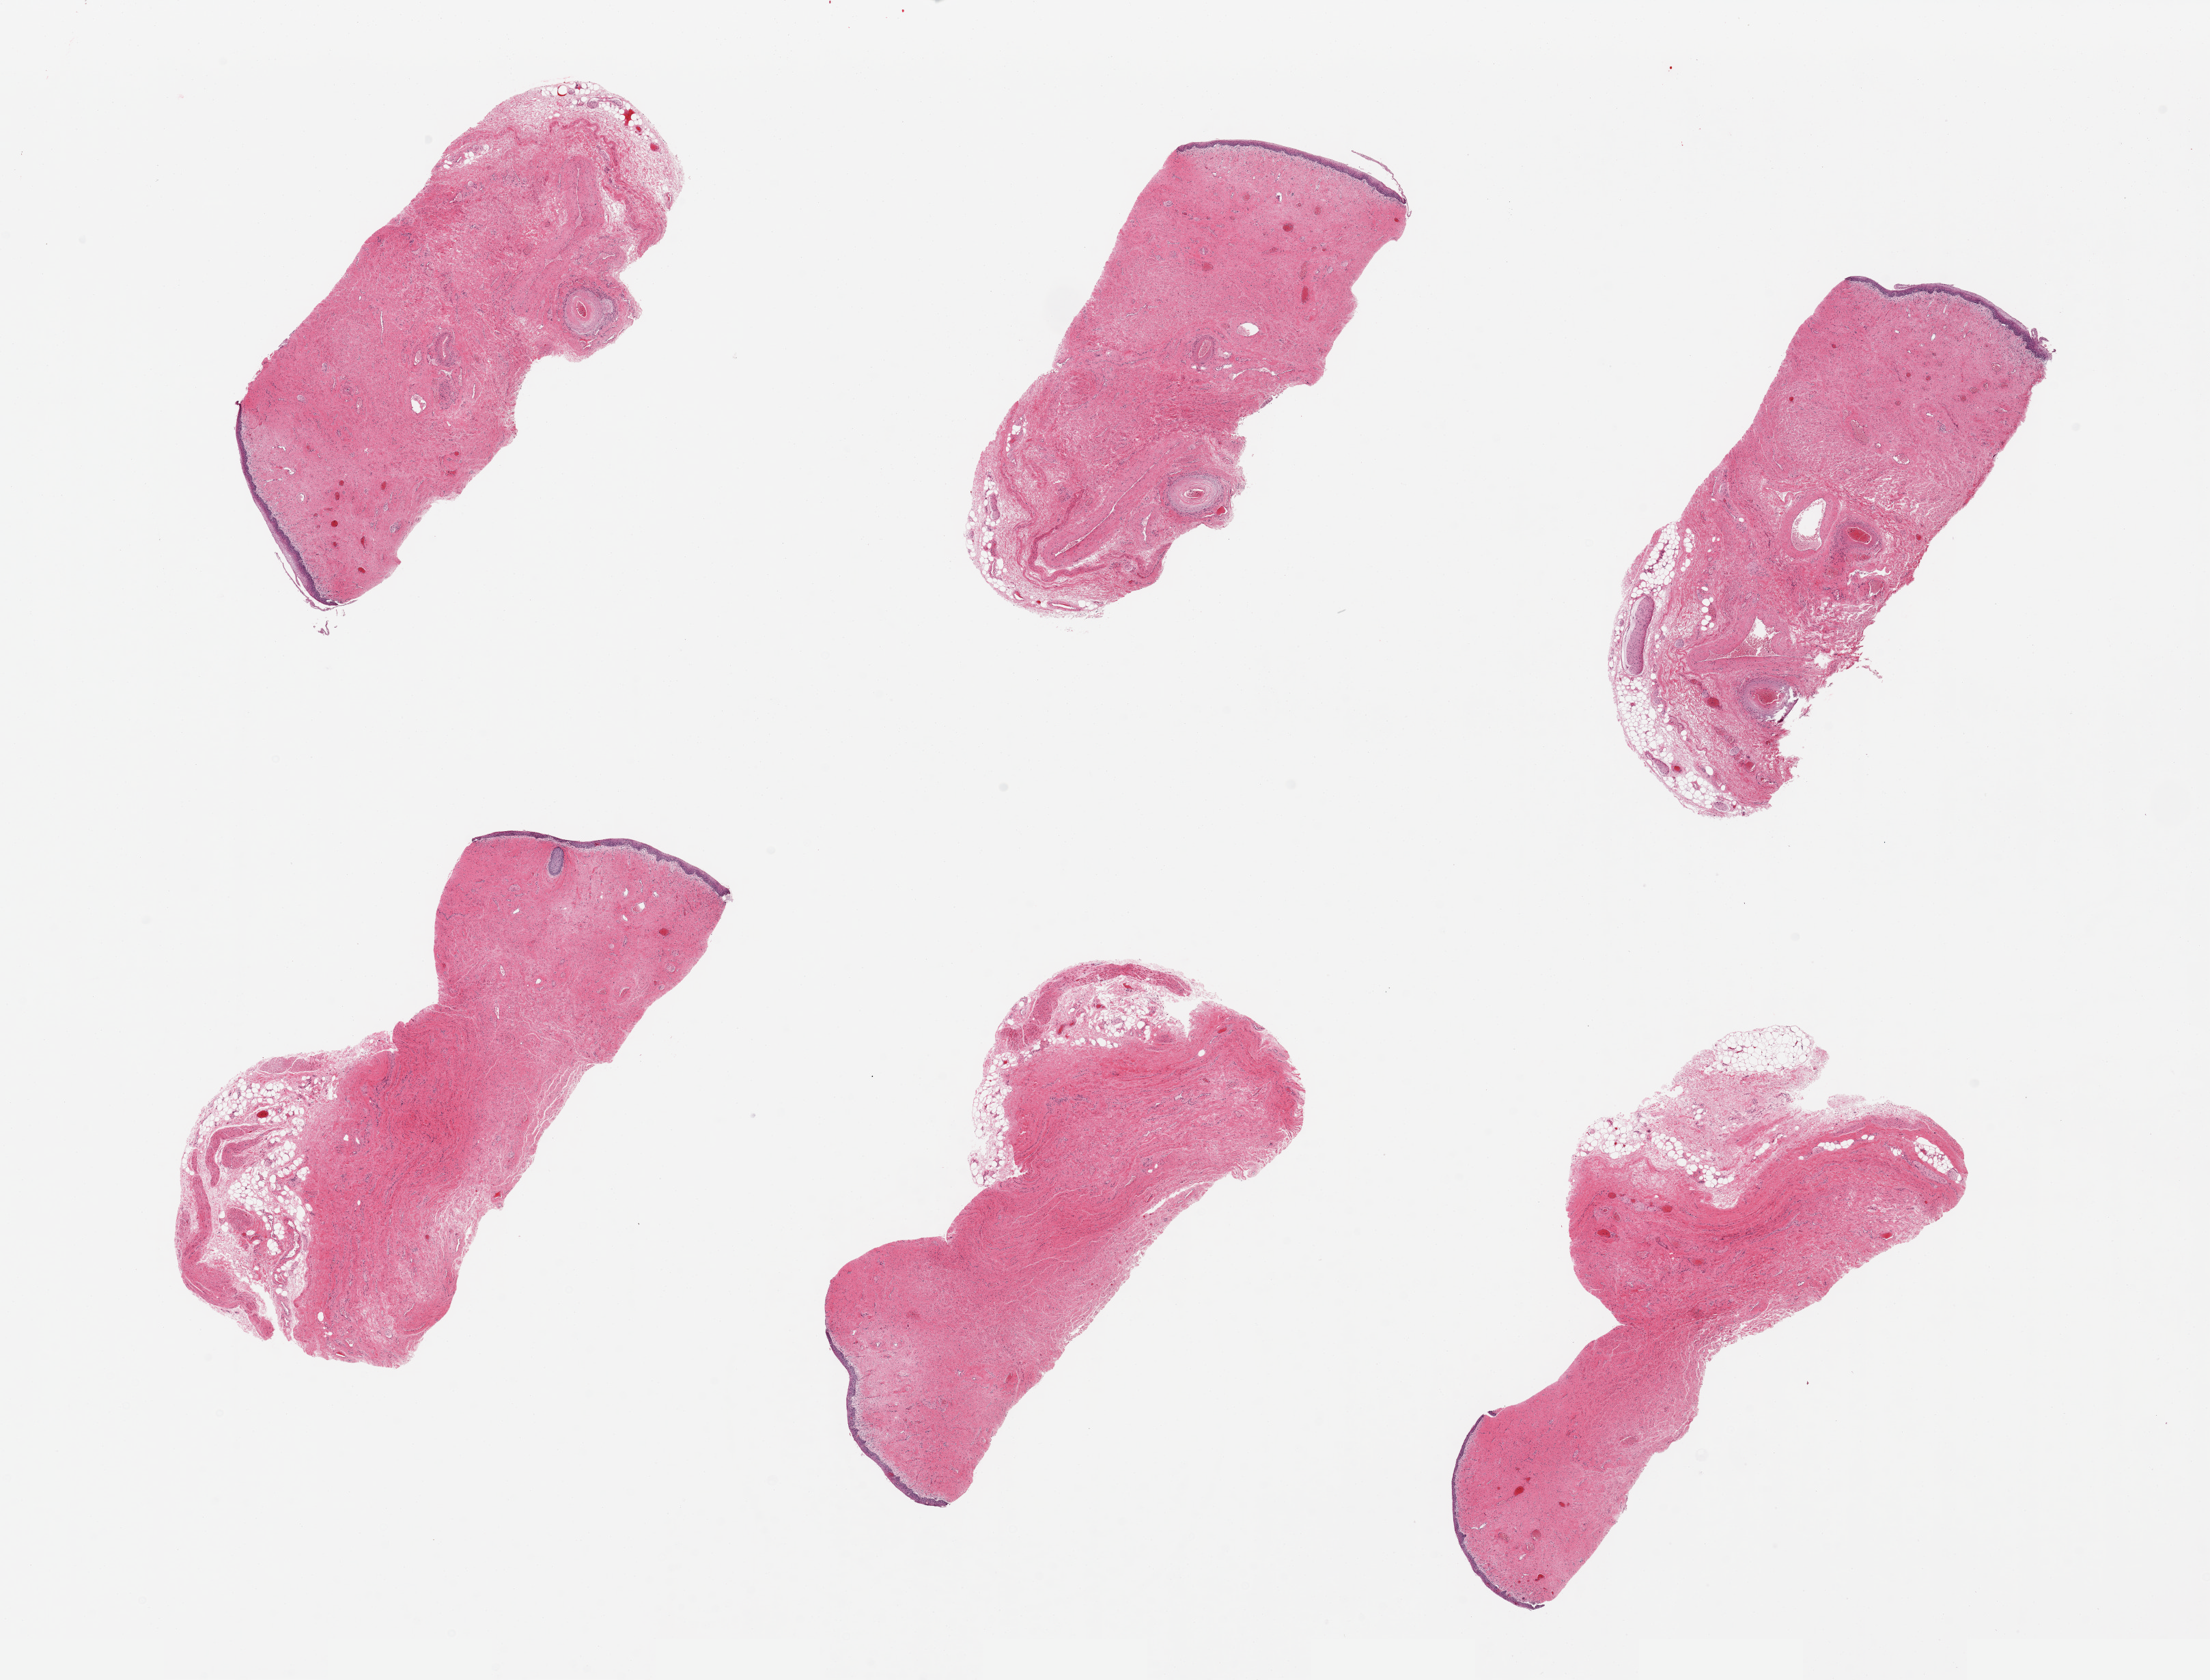
Digitized haematoxylin and eosin-stained section — whole scanned area (about 25.6 x 19.5 mm) shown as a low-resolution overview, PAXgene-fixed, paraffin-embedded tissue, target tissue: vagina, tissue donor sample. Female donor.
Review note (as recorded): 6 pieces, squamous mucosa is 0.1mm, ~1.5% thickness.